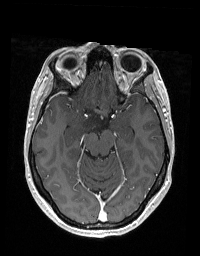
Brain MRI from a brain-tumour surgery series, one axial slice. Position 117 of 192 along the scan axis. T1-weighted post-contrast. 200 × 256 image matrix. From the clinical record (not read from this slice): histopathology: Glioblastoma; WHO grade: 2.
Structures marked on this image (outlined manually by an expert reader):
- tumour: box from (x=73, y=113) to (x=102, y=138) px